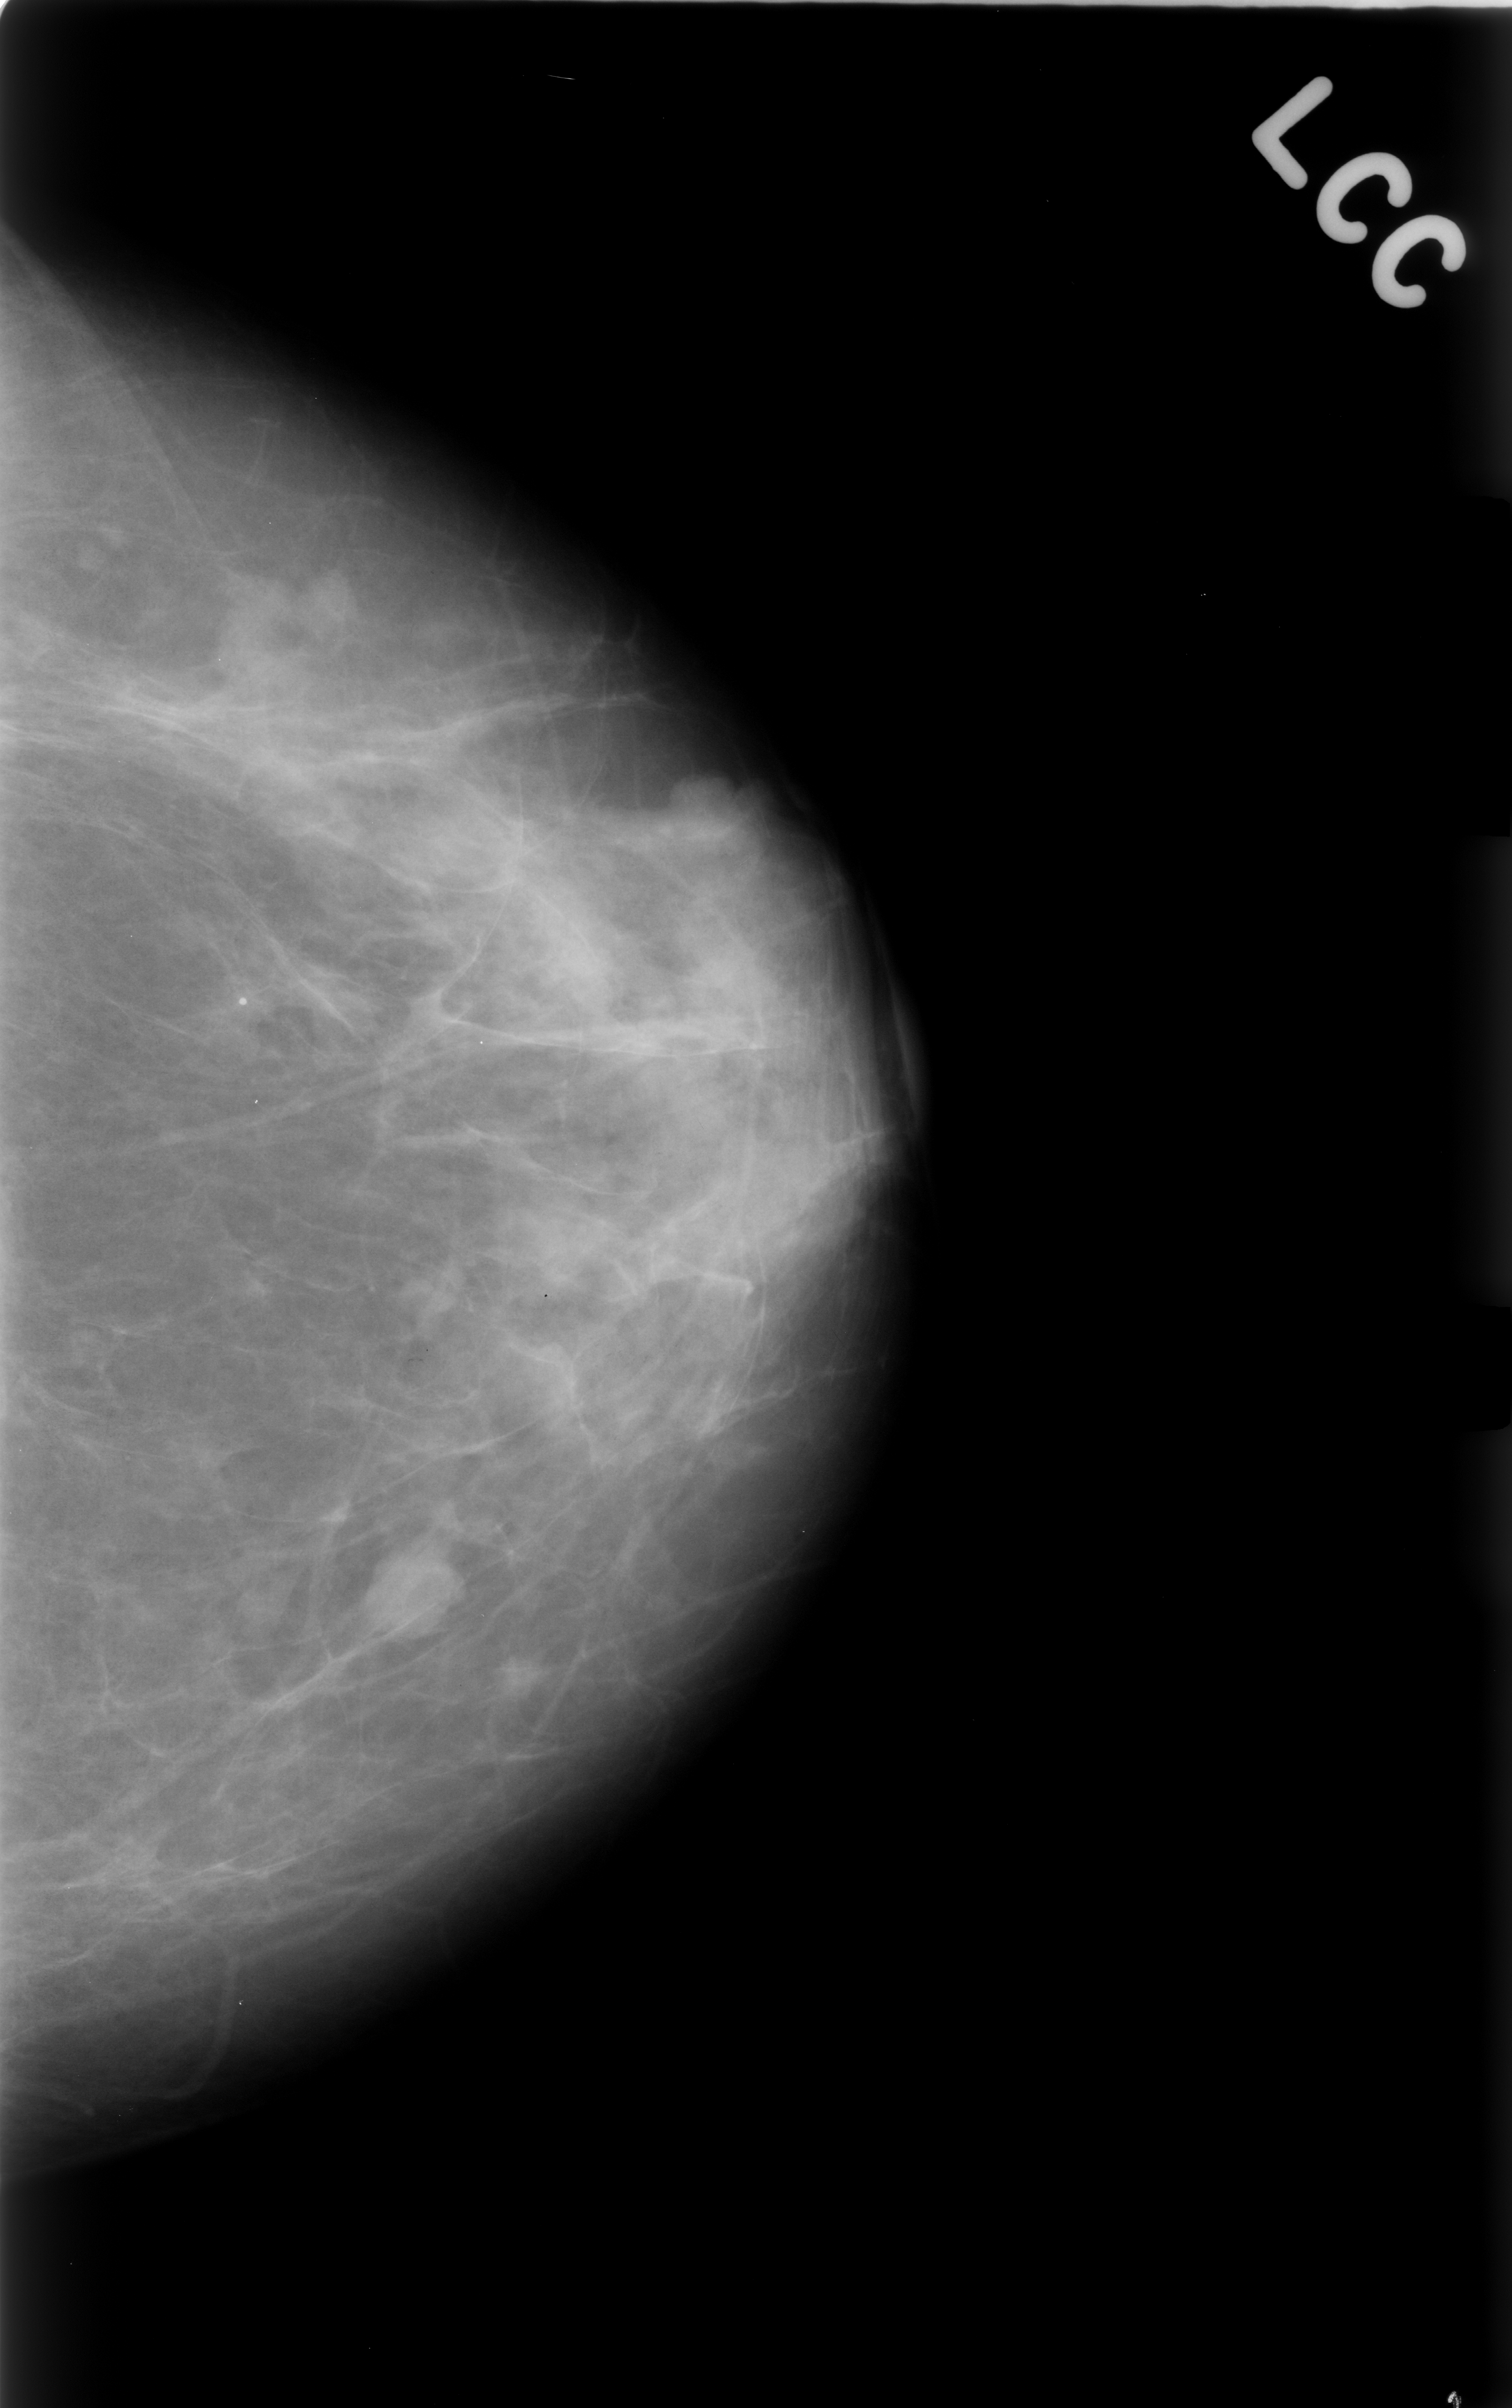
Scanned film-screen mammogram. Left breast. Craniocaudal (CC) view. BI-RADS breast density category 2 (scale 1–4). 1512 × 2408 image matrix.
Expert-marked regions of interest on this film, with their recorded descriptors:
- mass, shape lobulated, margins circumscribed; BI-RADS assessment category 4; pathology result (as recorded, not read from the image): benign: bounding box <346,1516,475,1654> (left, top, right, bottom; pixels)